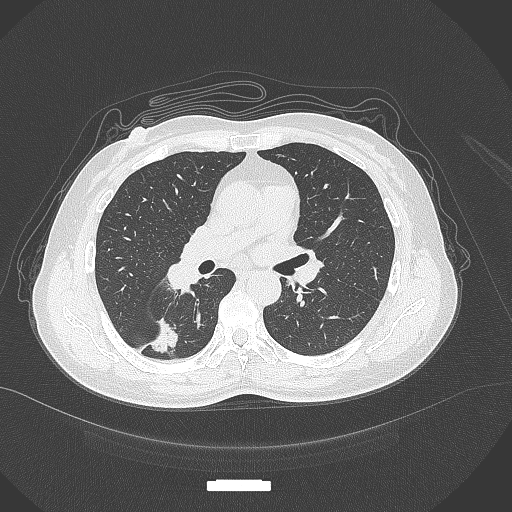
Chest CT, one axial slice. Position 170 of 352 along the scan axis. Reconstruction kernel B70f. 120 kVp. Lung window (W 1500 / L -600 HU). 512 × 512 image matrix. Female patient, age 55 years. From the clinical record (not read from this slice): clinical TNM (as recorded): T1c N1 M0.
Outlined on this slice (rectangle marked by the reading radiologist):
- lung tumour (recorded histology: adenocarcinoma): bounding box (x1, y1, x2, y2) in pixels: (146, 313, 183, 357)